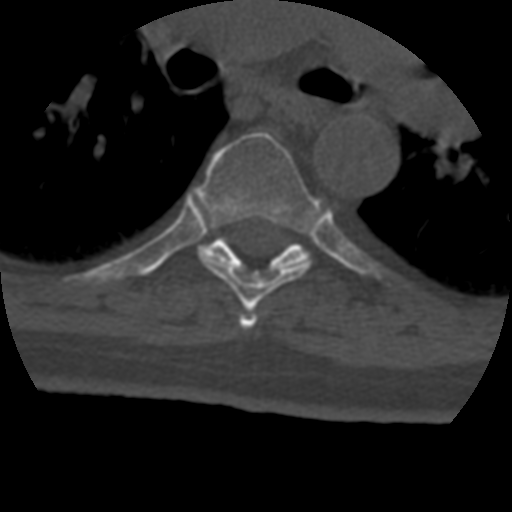
CT including the spine, one axial slice. Position 294 of 399 along the scan axis. Reconstruction kernel STANDARD. 120 kVp. Bone window (W 1800 / L 400 HU). 512 × 512 image matrix, field of view 160 × 160 mm. Patient age 69 years. From the clinical record (not read from this slice): primary cancer: prostate.
Outlined on this slice (semi-automatic segmentation, software-assisted and operator-edited):
- T5 vertebra: bounding box (x1, y1, x2, y2) in pixels: (239, 312, 257, 329)
- T6 vertebra: (198, 132, 321, 310)
- T7 vertebra: (208, 236, 310, 270)